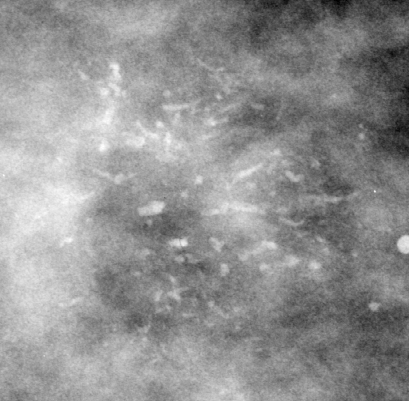
Cropped region of a digitized screen-film mammogram centred on a radiologist-marked abnormality; left breast; CC view.
- Marked abnormality: calcifications, morphology fine linear branching, distribution clustered; BI-RADS assessment category 5; subtlety rating 5 on a 1 (subtle) to 5 (obvious) scale; pathology result (as recorded, not read from the image): malignant.